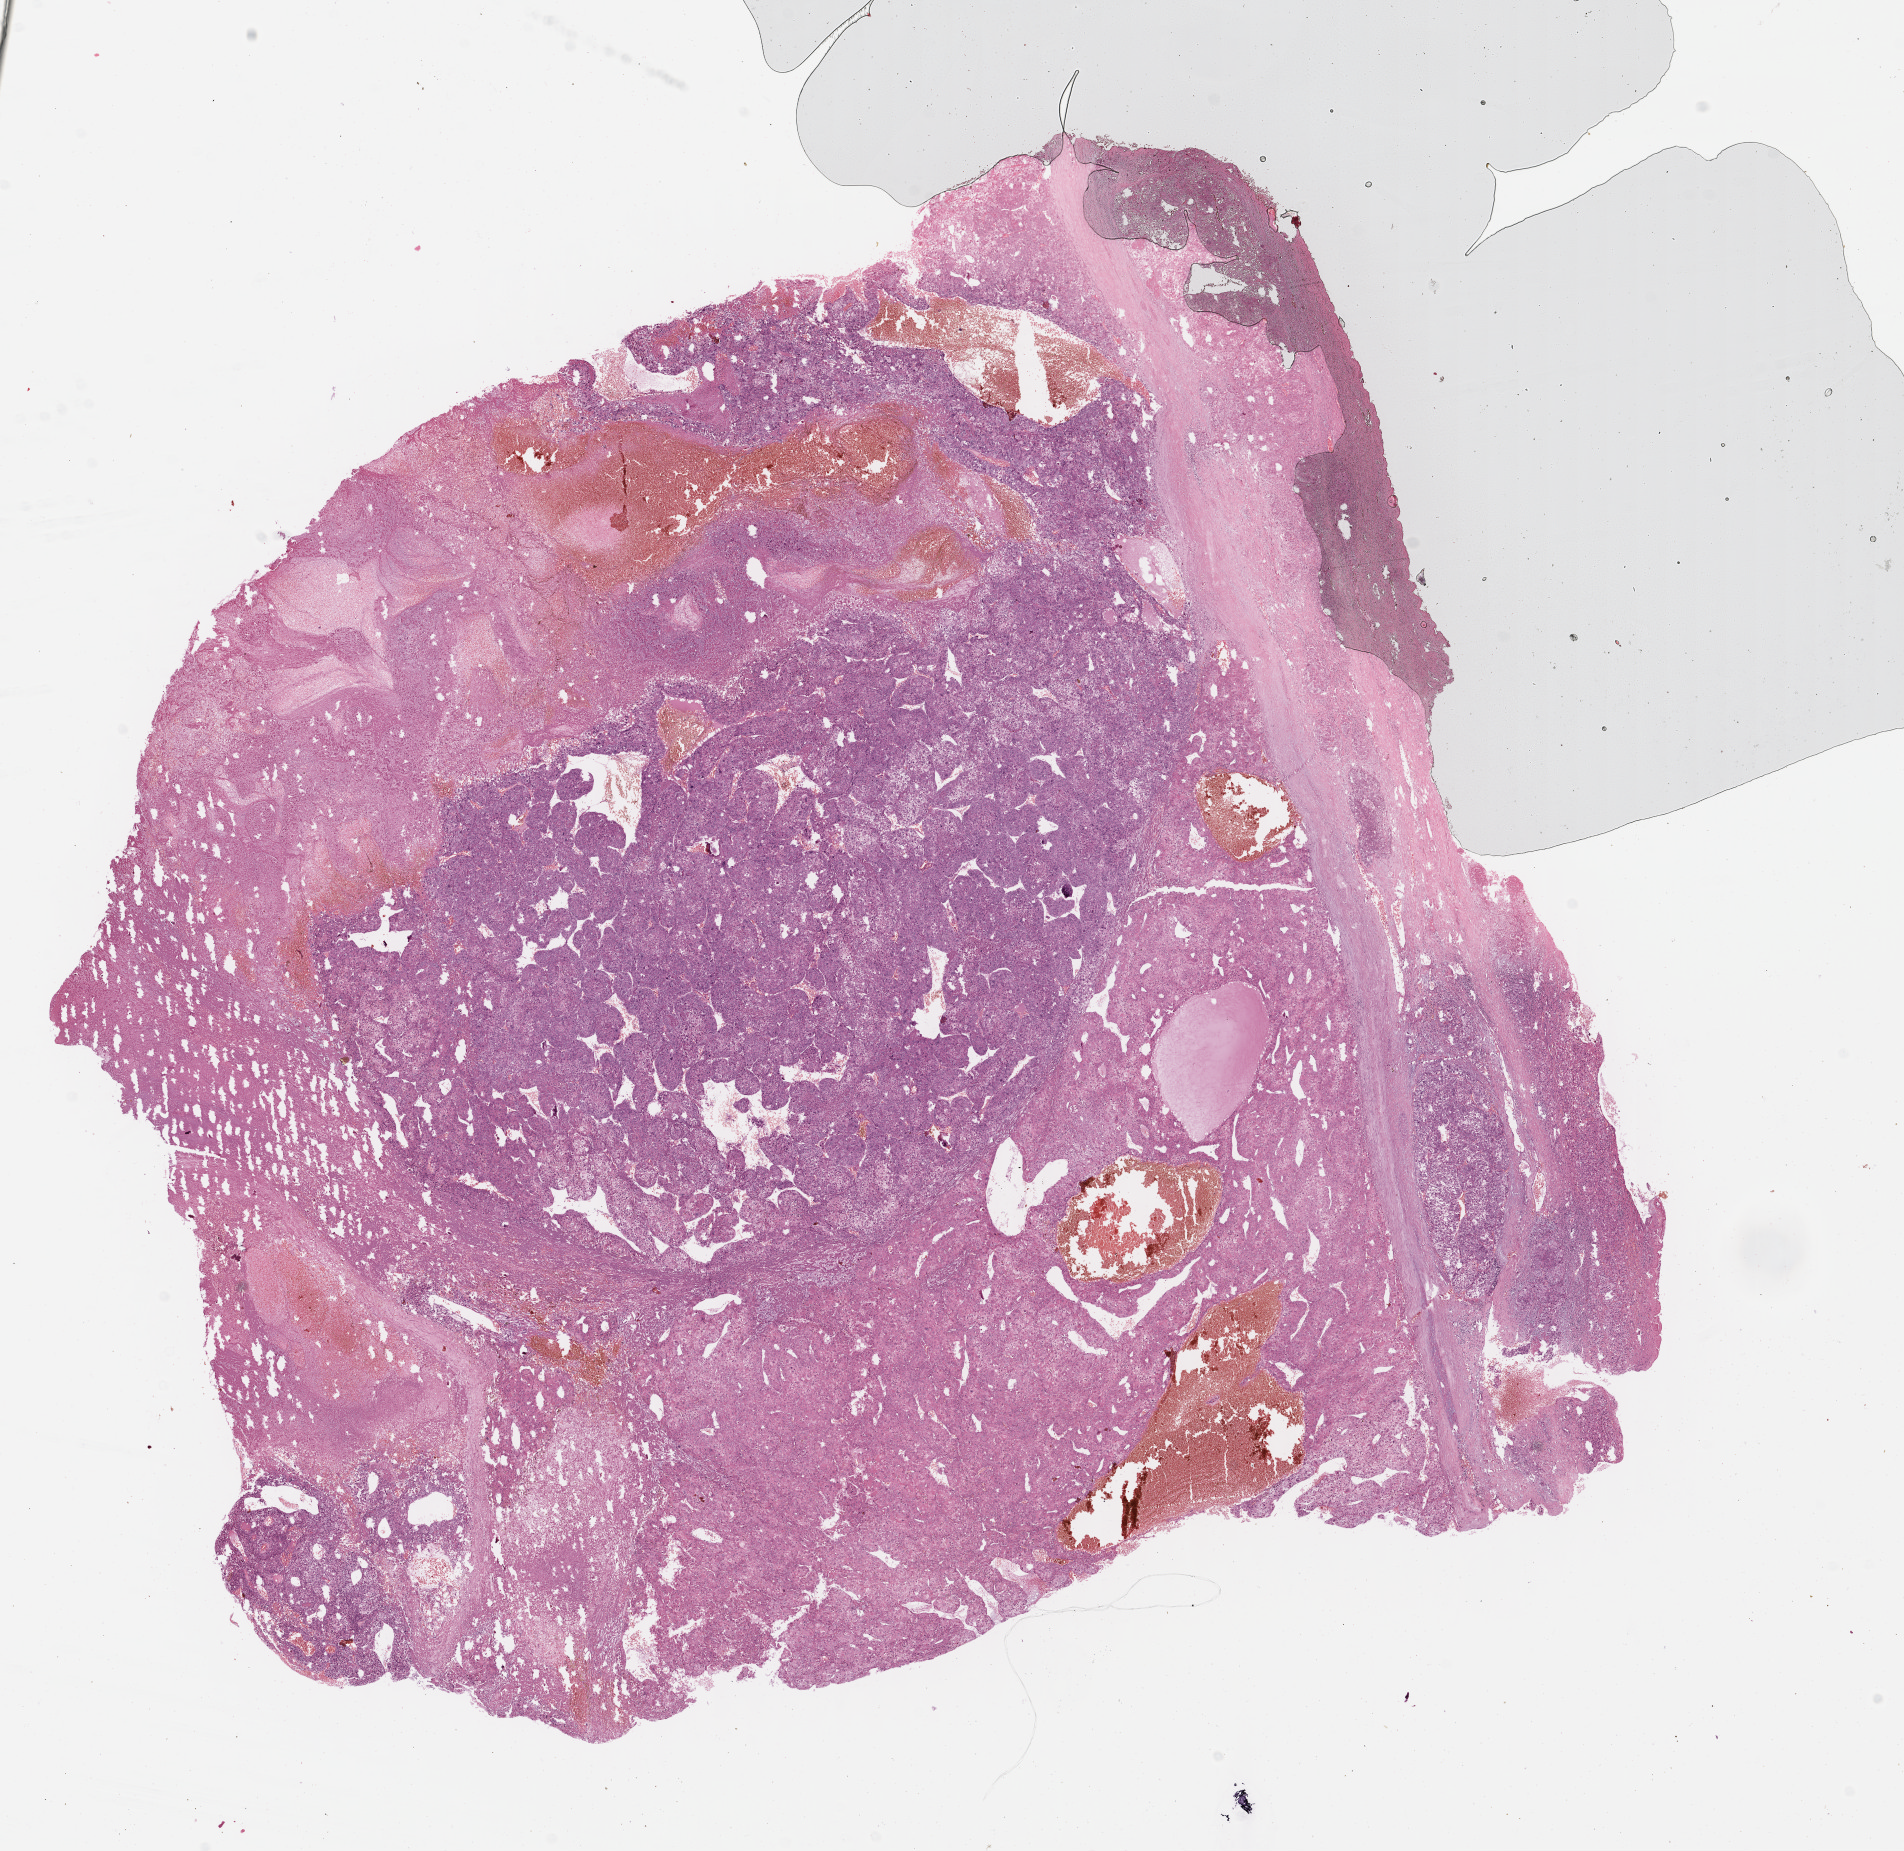
Whole-slide histology image, Hematoxylin and eosin (H&E) stained, whole scanned area (about 15.0 x 14.5 mm, acquisition: 40x scan) shown as a low-resolution overview. FFPE section. Primary tumour sample from the liver. Female, age 60 years at initial diagnosis. Histologic grade: G2 (moderately differentiated).
- diagnosis: Hepatocellular carcinoma, NOS
- AJCC pathologic stage: IIIC (7th edition)